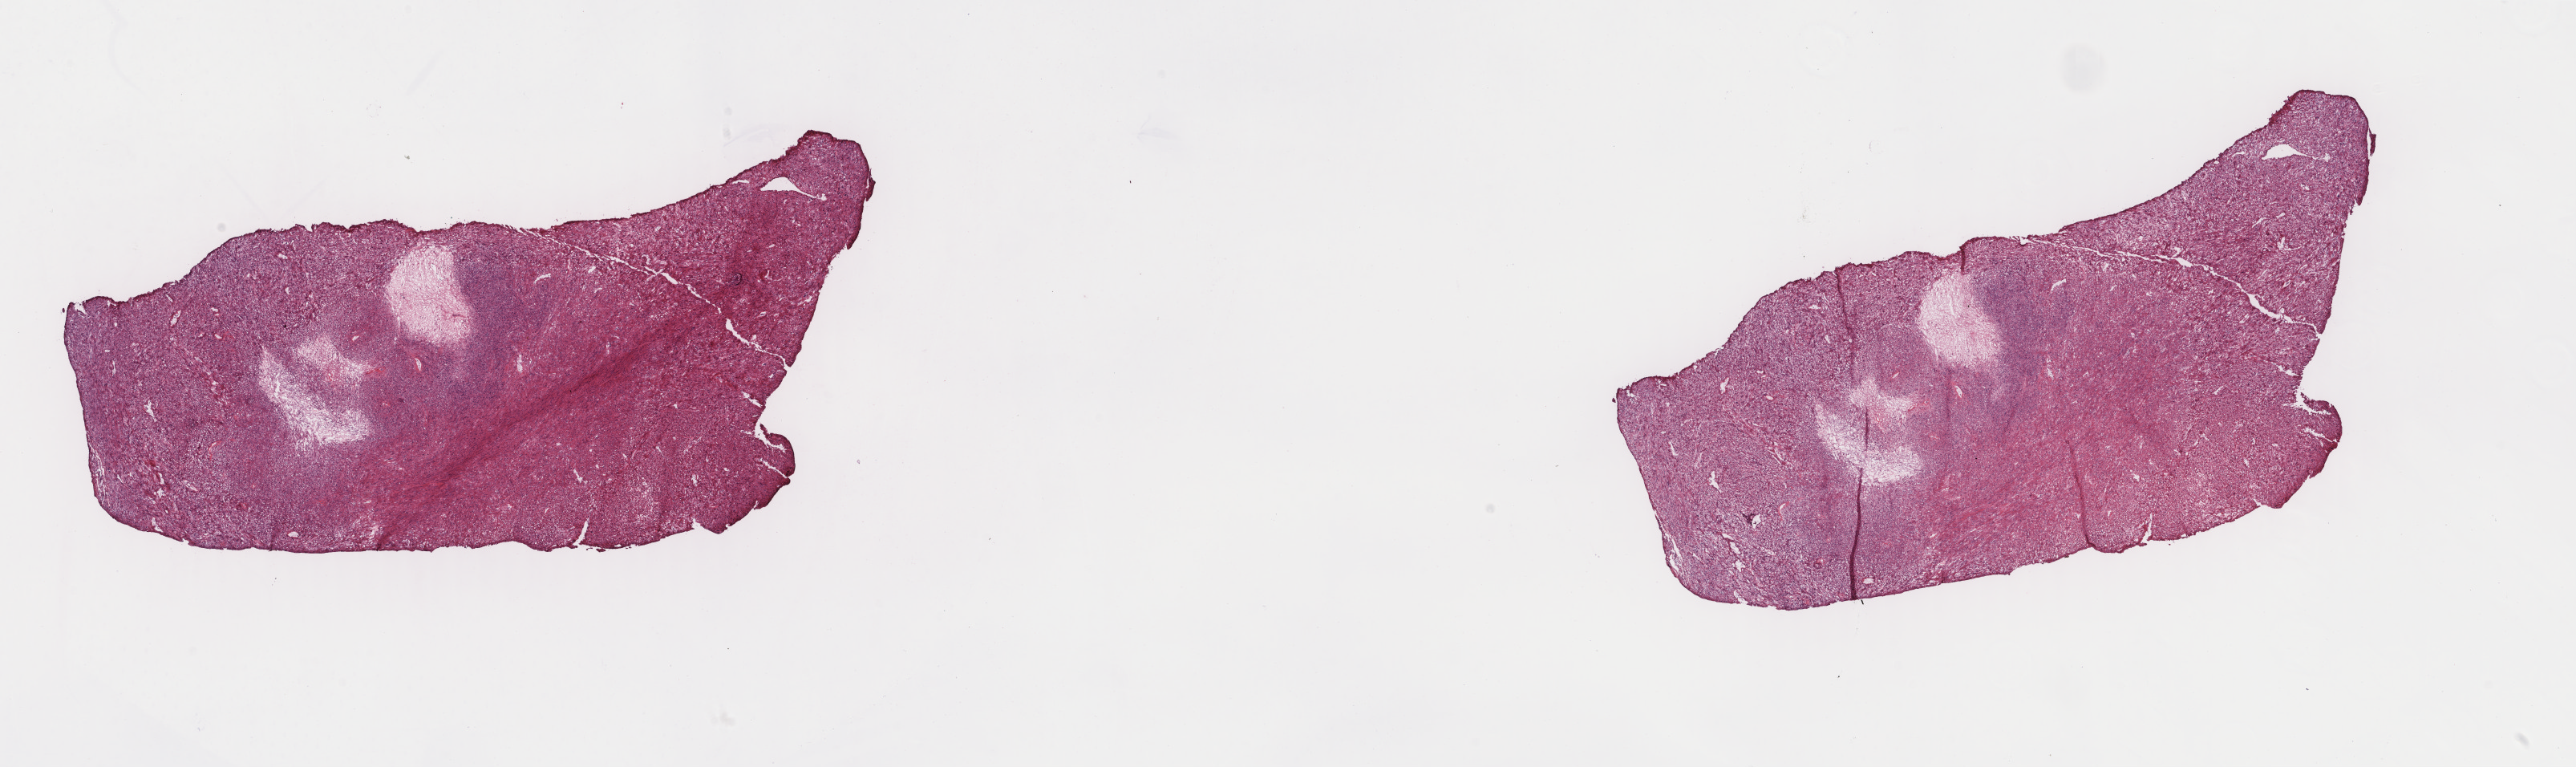
H&E-stained whole-slide image — shown as a low-resolution overview of the whole scanned area (about 25.5 x 7.6 mm); frozen section from the top of the tissue portion; sample: primary tumour, retroperitoneum and peritoneum. Patient: male, age at initial diagnosis 54 years. Slide review estimates, as recorded: tumour cells 90%, tumour nuclei 95%, normal cells 0%, stromal cells 10%, necrosis 0%. Inflammatory infiltration, as recorded: lymphocyte infiltration 0%, monocyte infiltration 0%, neutrophil infiltration 0%.
• pathologic diagnosis: Leiomyosarcoma, NOS (retroperitoneum)